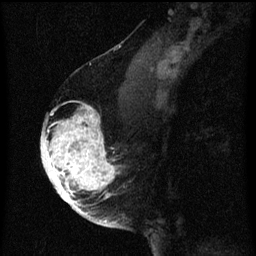
Breast MRI (dynamic contrast-enhanced), one sagittal slice. Slice 40 of 60 in the series (ordered by position). Dynamic contrast-enhanced series, image 2 of 3 at this slice position (ordered by acquisition). 1.5 T. TE 4.2 ms, TR 8 ms. 2 mm slice thickness. 256 × 256 image matrix. Female patient, age 56 years.
Structures marked on this image (semi-automatic segmentation, software-assisted and operator-edited):
- analysis volume of interest (the breast-tissue region the enhancement analysis was run in; not a lesion): bounding box <42,108,125,219> (left, top, right, bottom; pixels)
- tumour enhancement mask (voxels above the 70 % enhancement threshold inside the analysis volume of interest): <42,108,121,219>